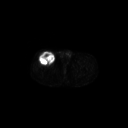
FDG PET of an extremity soft-tissue mass (from a PET/CT study), one axial slice; position 285 of 311 along the scan axis; 3.27 mm slice thickness; 128 × 128 image matrix, field of view 700 × 700 mm. Male patient, age 56 years. From the clinical record (not read from this slice): histological type: pleiomorphic leiomyosarcoma; grade: intermediate; site of the primary tumour: right thigh.
Outlined on this slice (expert contour drawn on MRI and transferred to this co-registered scan by the dataset authors):
- gross tumour volume including surrounding oedema: bounding box [x1, y1, x2, y2] px = [38, 52, 55, 65]
- gross tumour volume (mass): [38, 52, 55, 65]